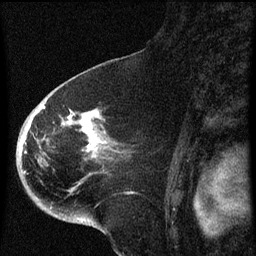
Breast MRI (dynamic contrast-enhanced), one sagittal slice. Slice 41 of 60 in the series (ordered by position). Dynamic contrast-enhanced series, image 2 of 4 at this slice position (ordered by acquisition). 1.5 T. TE 4.2 ms, TR 8 ms. 2 mm slice thickness. 256 × 256 image matrix, field of view 180 × 180 mm. Patient: female, 71 years.
Outlined on this slice (semi-automatically segmented with operator editing):
- analysis volume of interest (the breast-tissue region the enhancement analysis was run in; not a lesion): bounding box (x1, y1, x2, y2) in pixels: (32, 86, 132, 205)
- tumour enhancement mask (voxels above the 70 % enhancement threshold inside the analysis volume of interest): (39, 106, 99, 157)